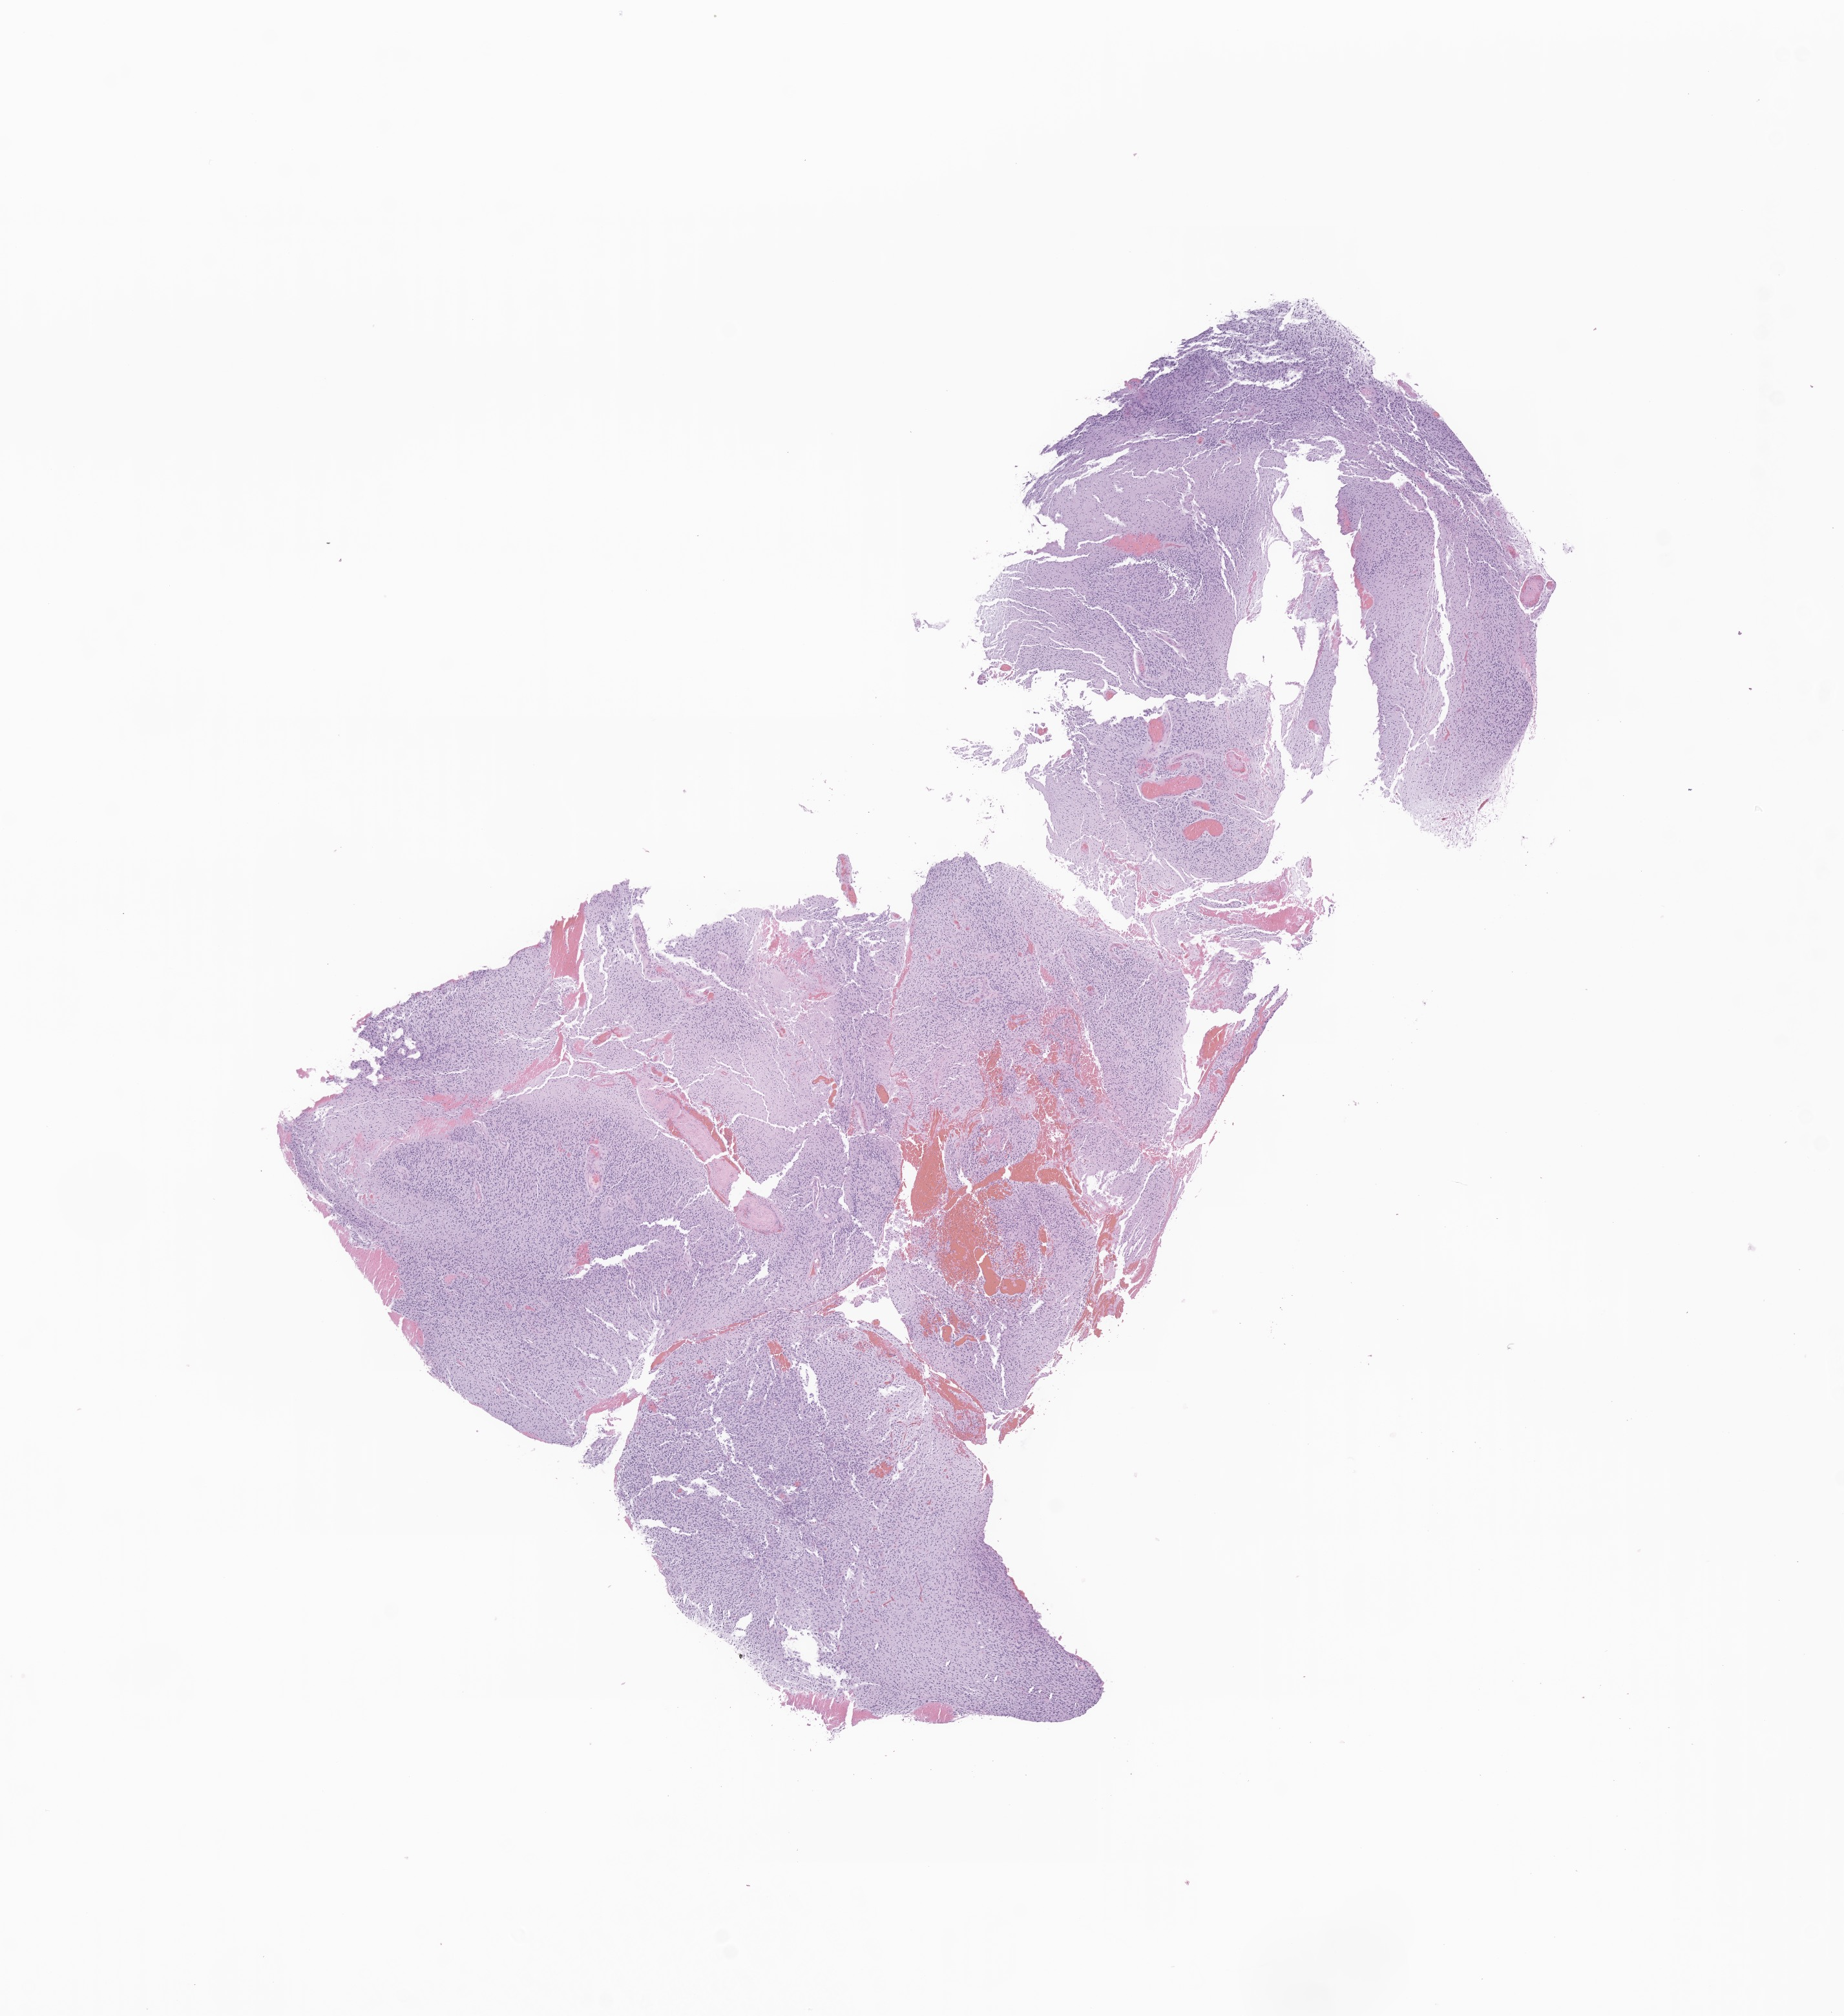
Whole-slide image, hematoxylin and eosin (H&E) stain of tumor tissue from the brain stem, shown as a low-resolution overview of the whole scanned area (about 12.0 x 13.2 mm); formalin-fixed paraffin-embedded section. Patient male; age 47 months.
• recorded diagnosis: Glioma, malignant